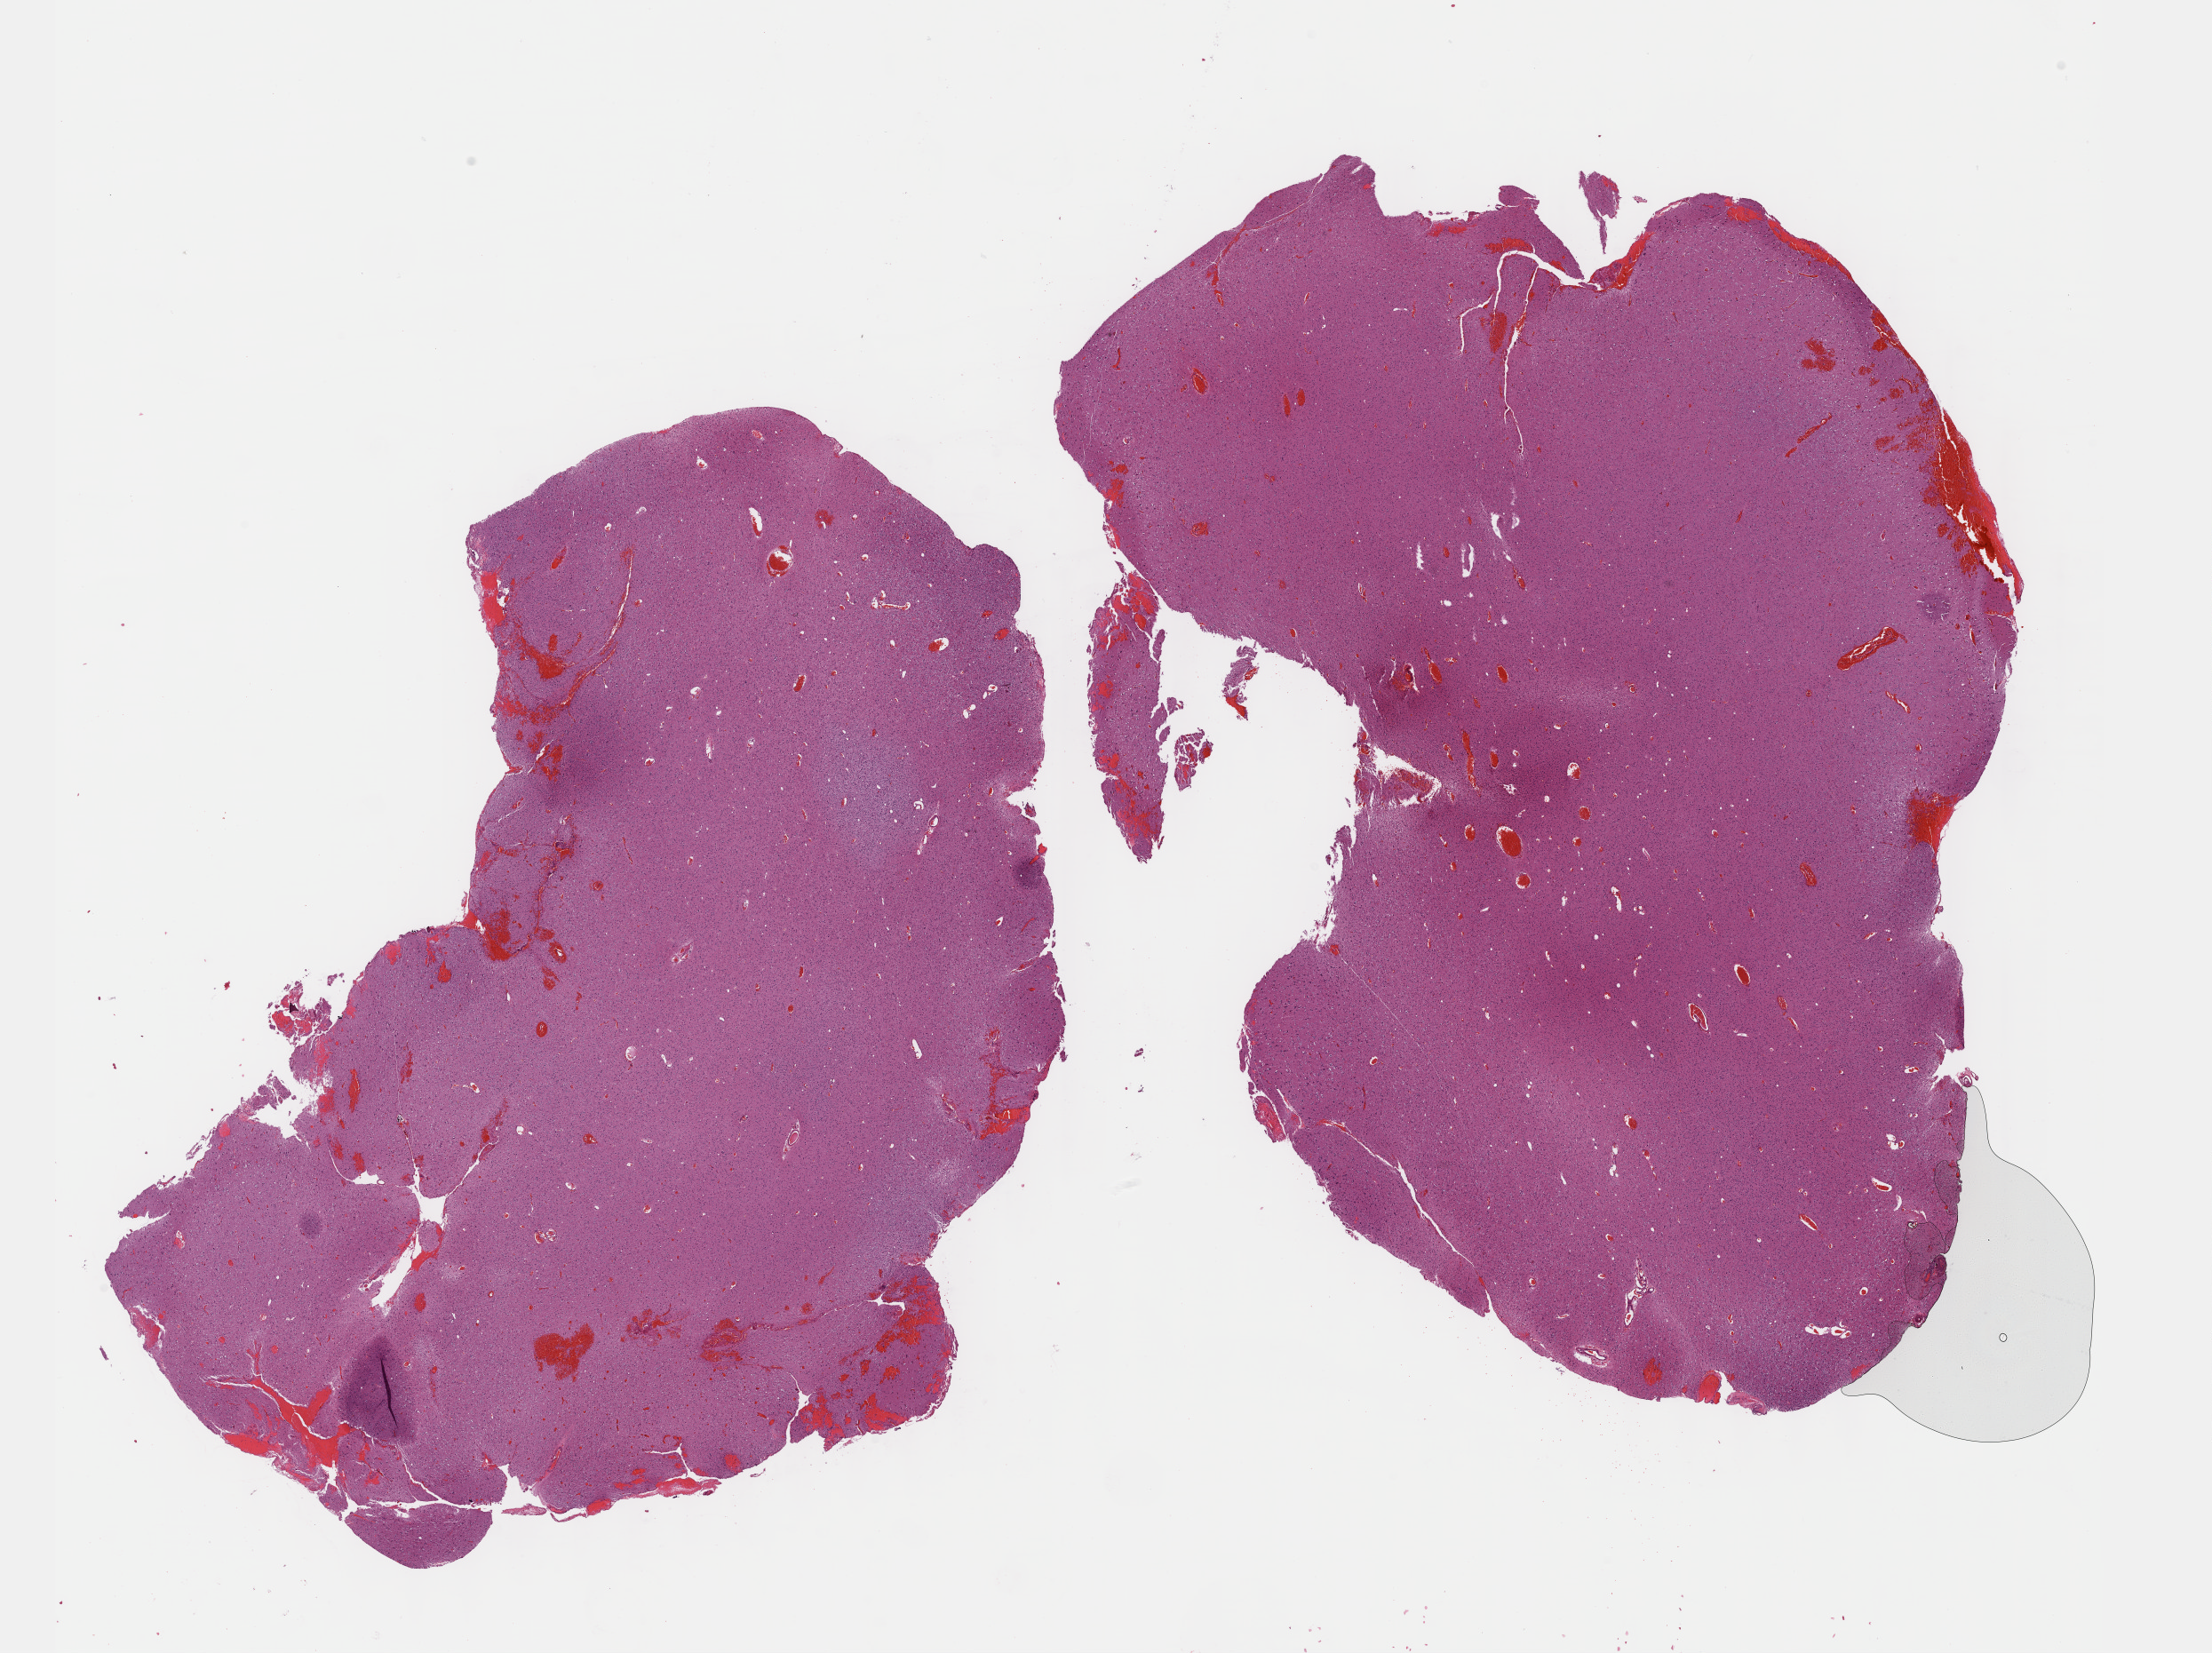
Digitized H&E tissue section (whole slide) — whole scanned area (about 20.1 x 15.0 mm, acquisition: 40x scan) shown as a low-resolution overview. Formalin-fixed paraffin-embedded (FFPE) diagnostic section. Brain, primary tumour sample. Patient: male, age at initial diagnosis 38 years. Histologic grade: G2 (moderately differentiated).
- laterality: left
- diagnosis: Oligodendroglioma, NOS